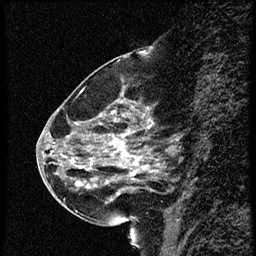
Breast MRI (dynamic contrast-enhanced), one sagittal slice; dynamic contrast-enhanced study with each time point stored as its own series, time point 2 of 4 at this slice position (early post-contrast, ordered by acquisition time); 1.5 T; TE 4.2 ms, TR 18.9 ms; 2 mm slice thickness; 256 × 256 image matrix. Female patient. Case-level facts recorded for this patient, not image findings: setting: breast cancer imaged before/during neoadjuvant chemotherapy; receptor status: HER2-positive.
Structures marked on this image (semi-automatic segmentation, software-assisted and operator-edited):
- analysis volume of interest (the breast-tissue region the enhancement analysis was run in; not a lesion): bounding box [x1, y1, x2, y2] px = [63, 80, 168, 215]
- tumour enhancement mask (voxels above the 100 % enhancement threshold inside the analysis volume of interest): [77, 112, 145, 195]